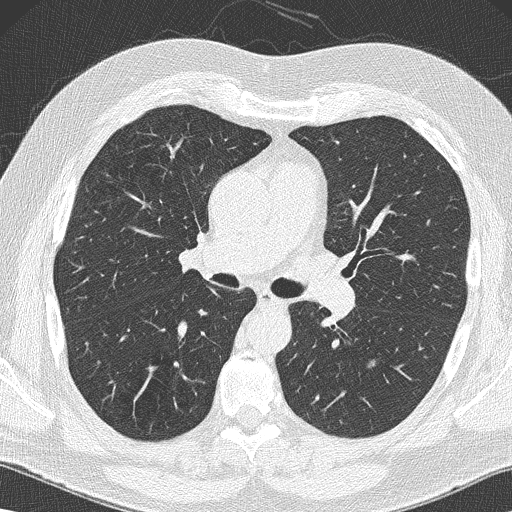
Chest CT (low-dose screening protocol), one axial image, baseline screening round, lung window (W 1500 / L -600 HU), slice 68 of 152 in the series. Male, age 59 years at enrolment.
Expert-annotated lung lesion, bounding box [x1, y1, x2, y2] px = [348, 349, 391, 384]. The screening reader recorded 2 non-calcified nodules or masses ≥4 mm on this exam (left lower lobe, left lower lobe); which of them this box marks is not recorded. Official screen result: positive, change unspecified: nodule(s) >= 4 mm or enlarging nodule(s), mass(es), or other non-specific abnormalities suspicious for lung cancer. Participant outcome: lung cancer diagnosed 61 days after this screen — large cell carcinoma, NOS, left lower lobe, poorly differentiated (G3), stage IA (AJCC 6th edition), 14 mm at pathology.